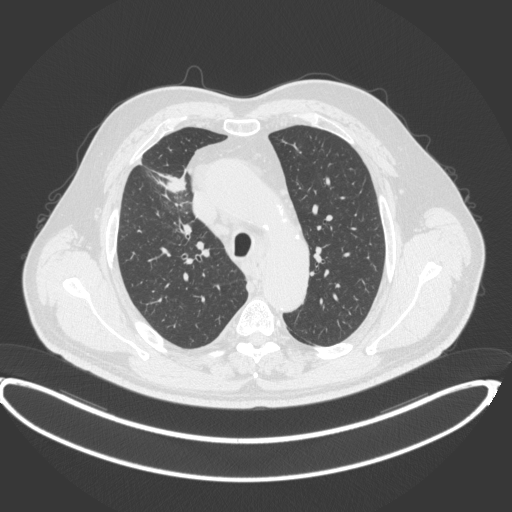
Chest CT, one axial slice. Position 301 of 395 along the scan axis. 120 kVp. Lung window (W 1500 / L -600 HU). 1 mm slice thickness. 512 × 512 image matrix, field of view 448 × 448 mm. Male patient, age 62 years. Case-level facts recorded for this patient, not image findings: clinical TNM (as recorded): T1c N3 M1c.
Structures marked on this image (bounding box drawn by a radiologist):
- lung tumour (recorded histology: adenocarcinoma): bounding box <161,169,190,193> (left, top, right, bottom; pixels)